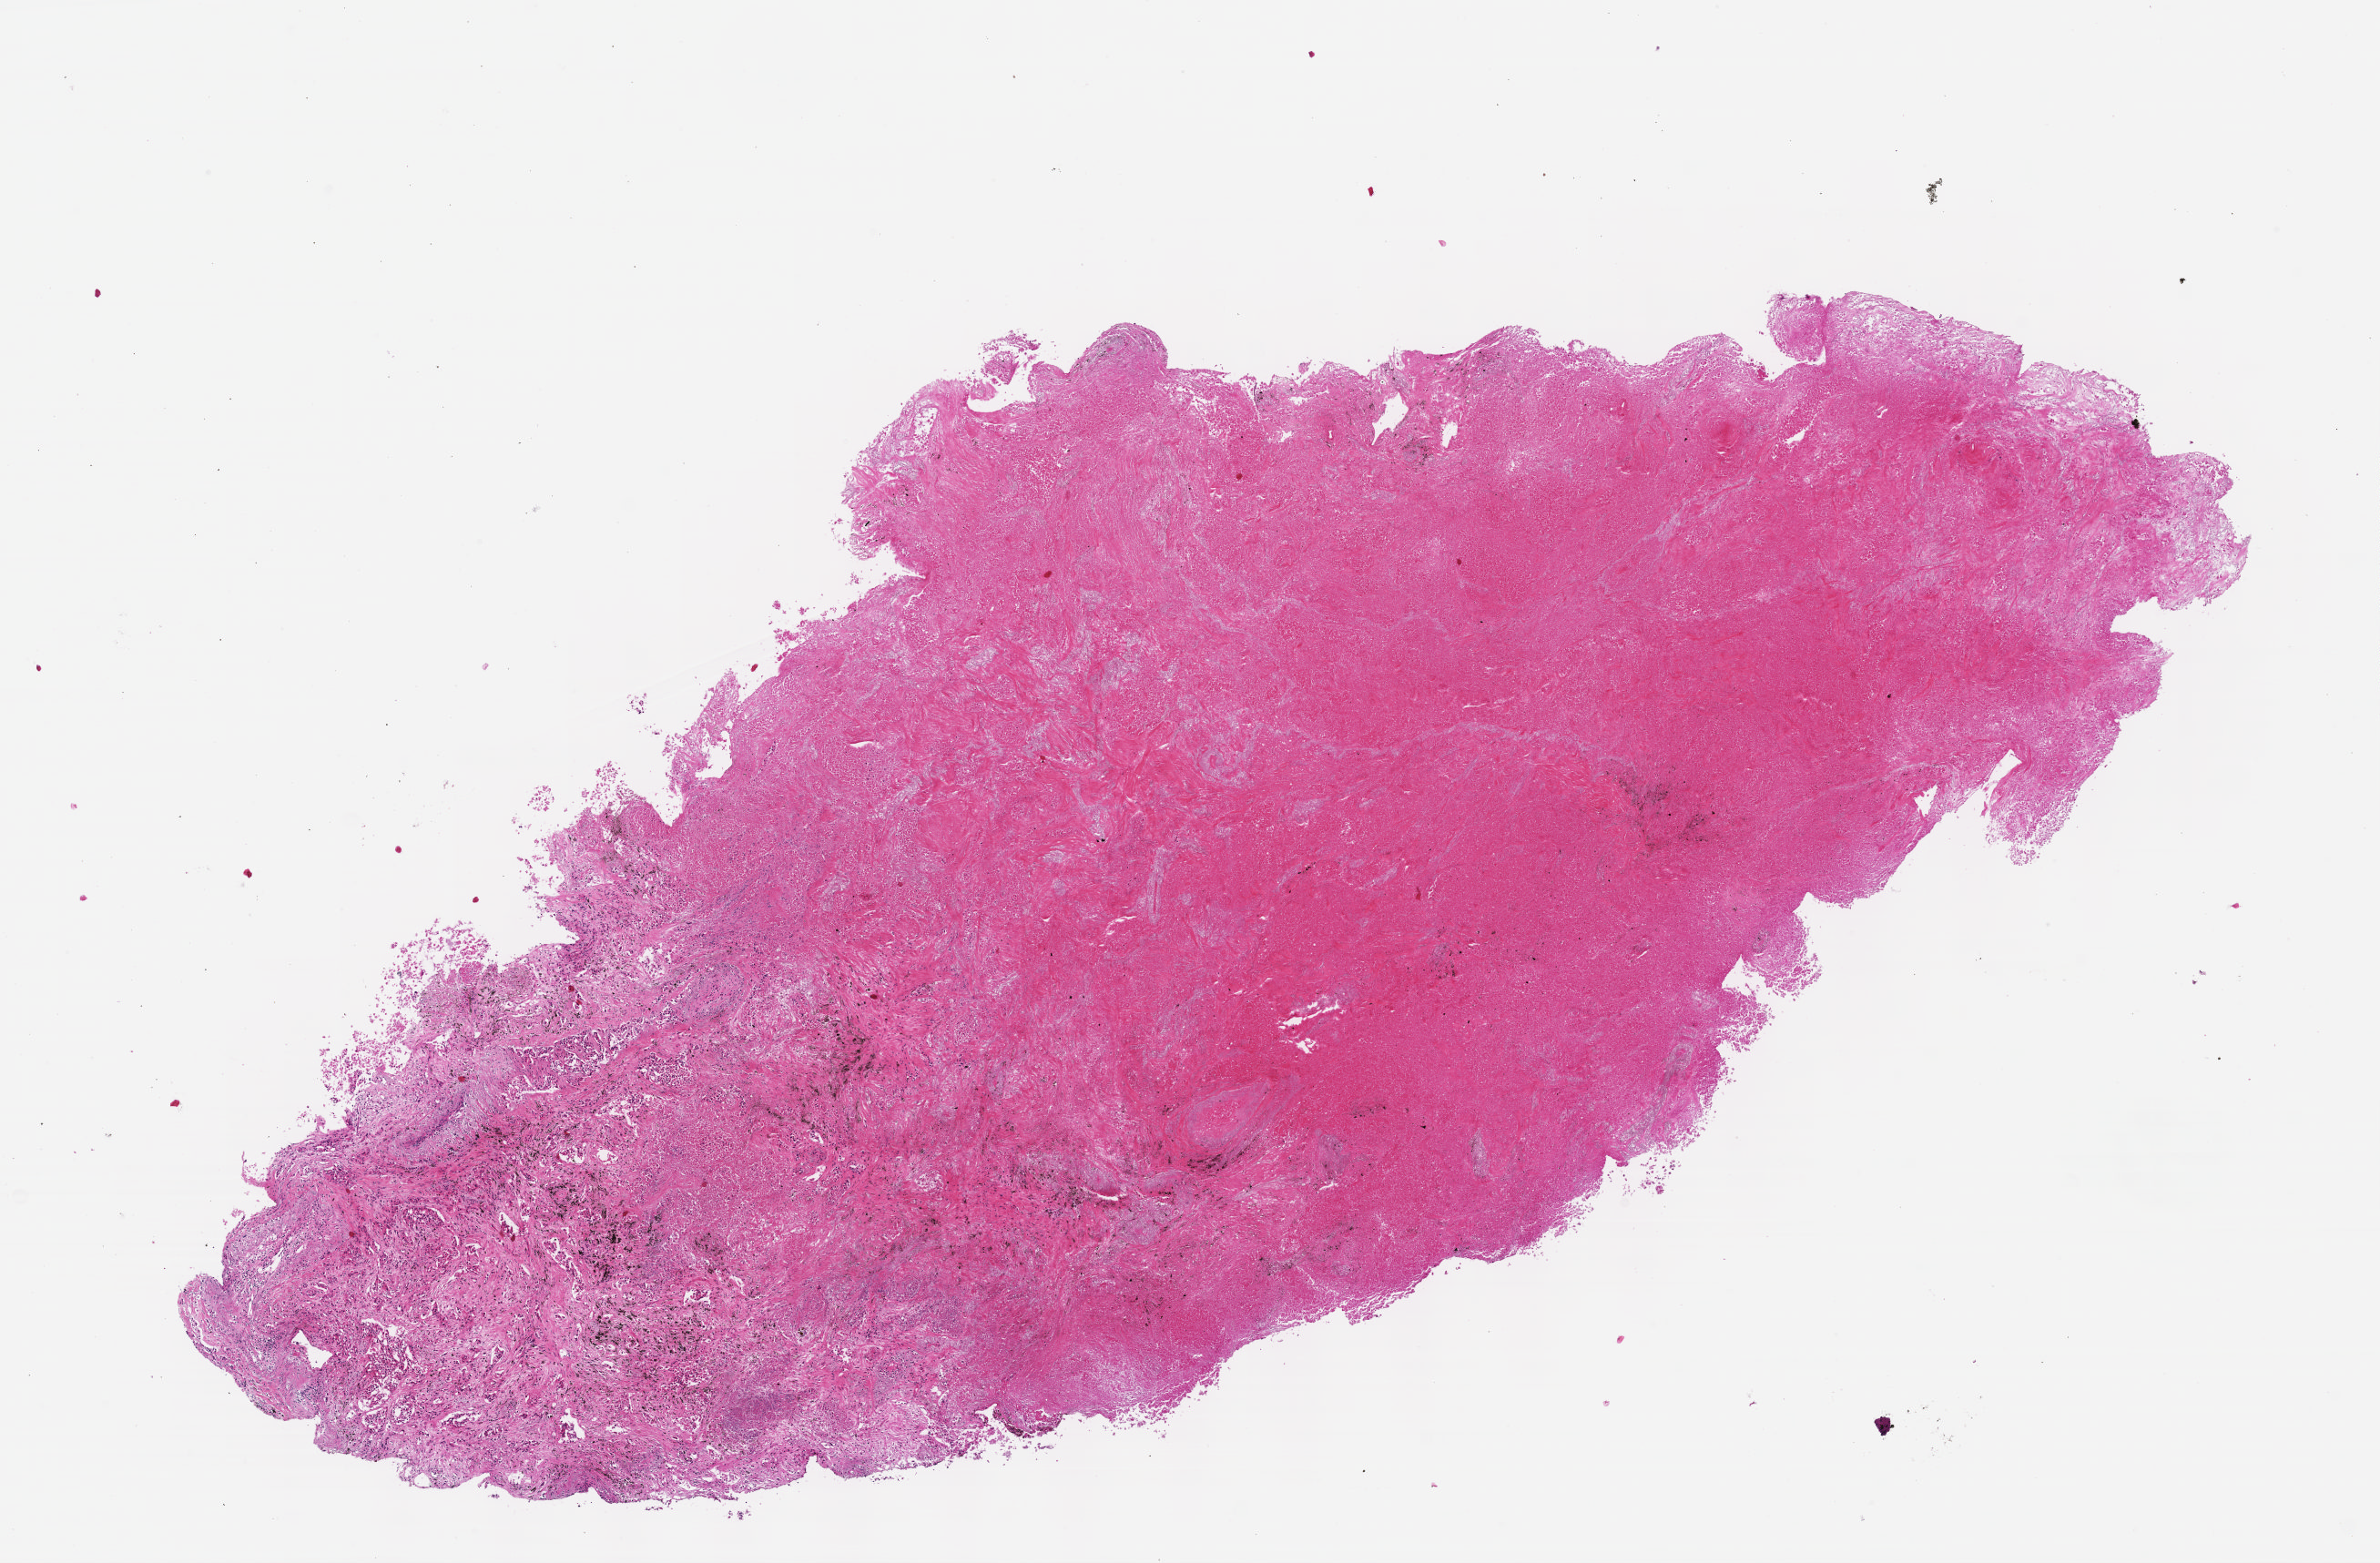
Digitized H&E tissue section (whole slide) — a low-resolution overview of the entire scanned area, about 10.6 x 6.9 mm (from a 40x scan). FFPE section. Primary tumour sample from the lung. Male, age 61 years at initial diagnosis.
Pathologic diagnosis: Adenocarcinoma, NOS.